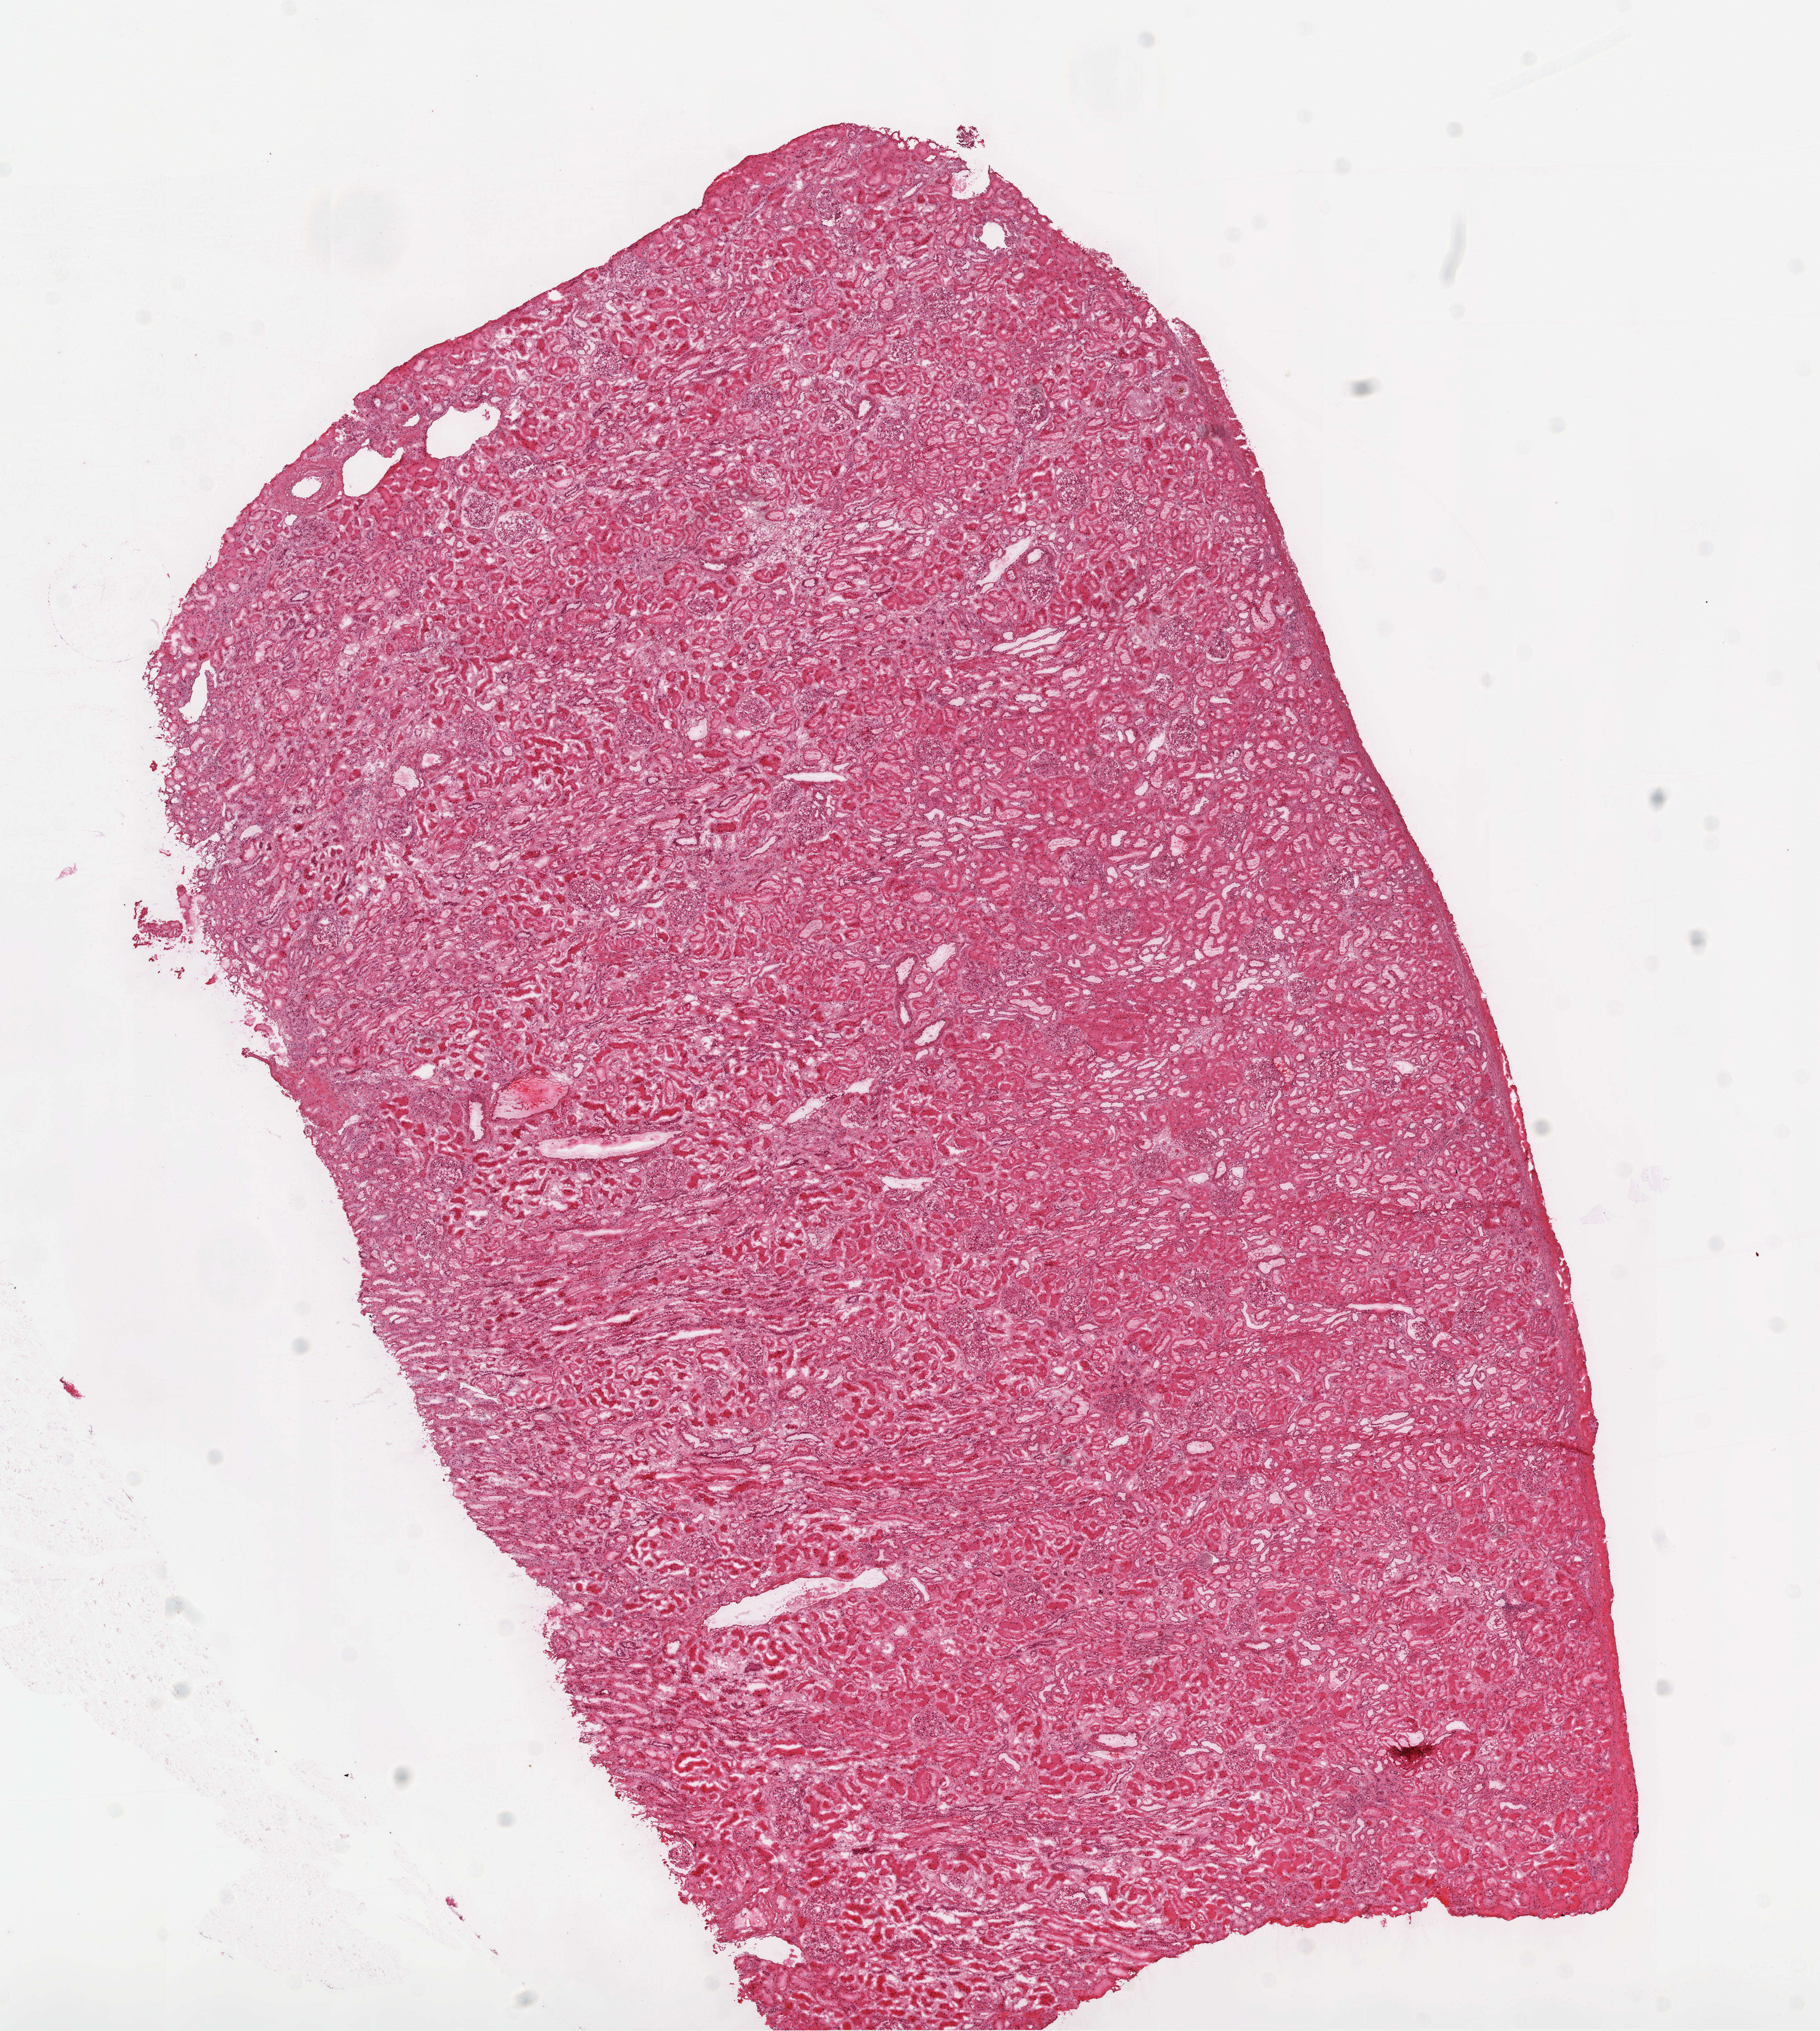
H&E whole-slide image — a low-resolution overview of the entire scanned area, about 11.0 x 12.3 mm. Frozen section. Kidney, solid tissue normal (non-tumour tissue) sample. Male patient; age at initial diagnosis 64 years.
• this section: solid tissue normal sample (biorepository sample class)
• patient diagnosis: Clear cell adenocarcinoma, NOS